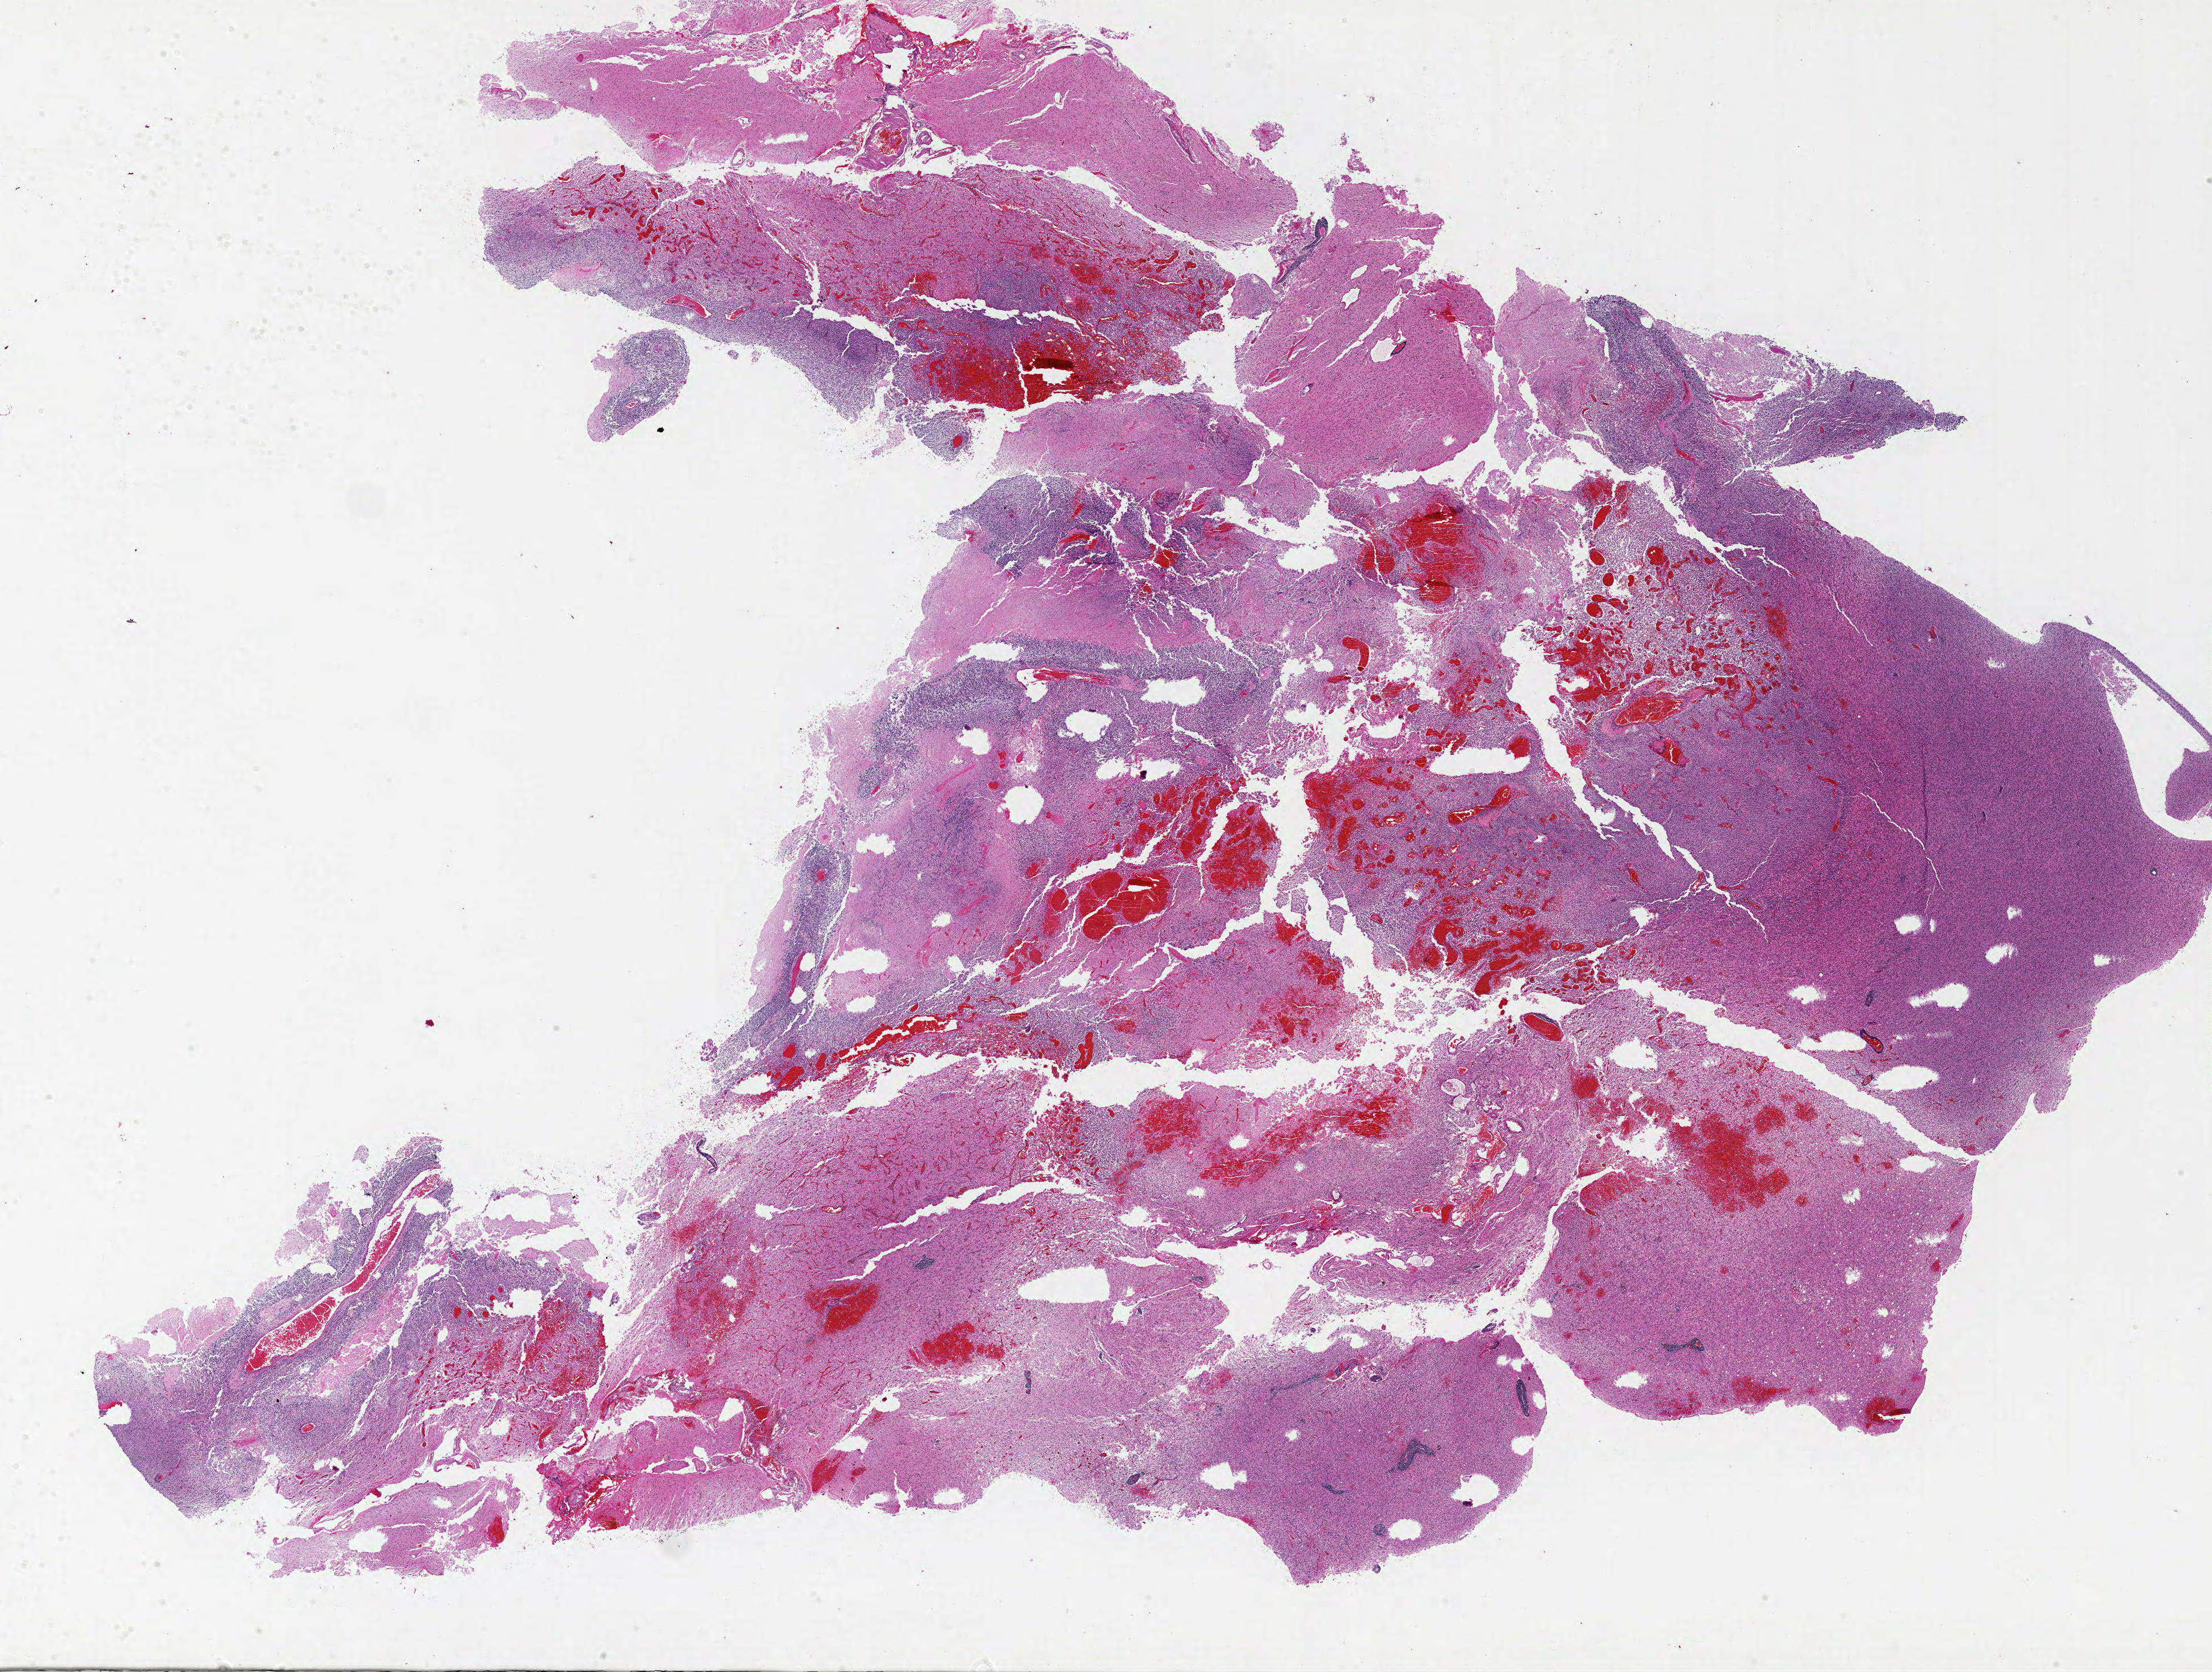
H&E whole-slide image, a low-resolution overview of the entire scanned area, about 31.0 x 23.4 mm. Formalin-fixed paraffin-embedded (FFPE) diagnostic section. Sample: primary tumour, brain. Male, age 75 years at initial diagnosis.
- pathologic diagnosis: Glioblastoma